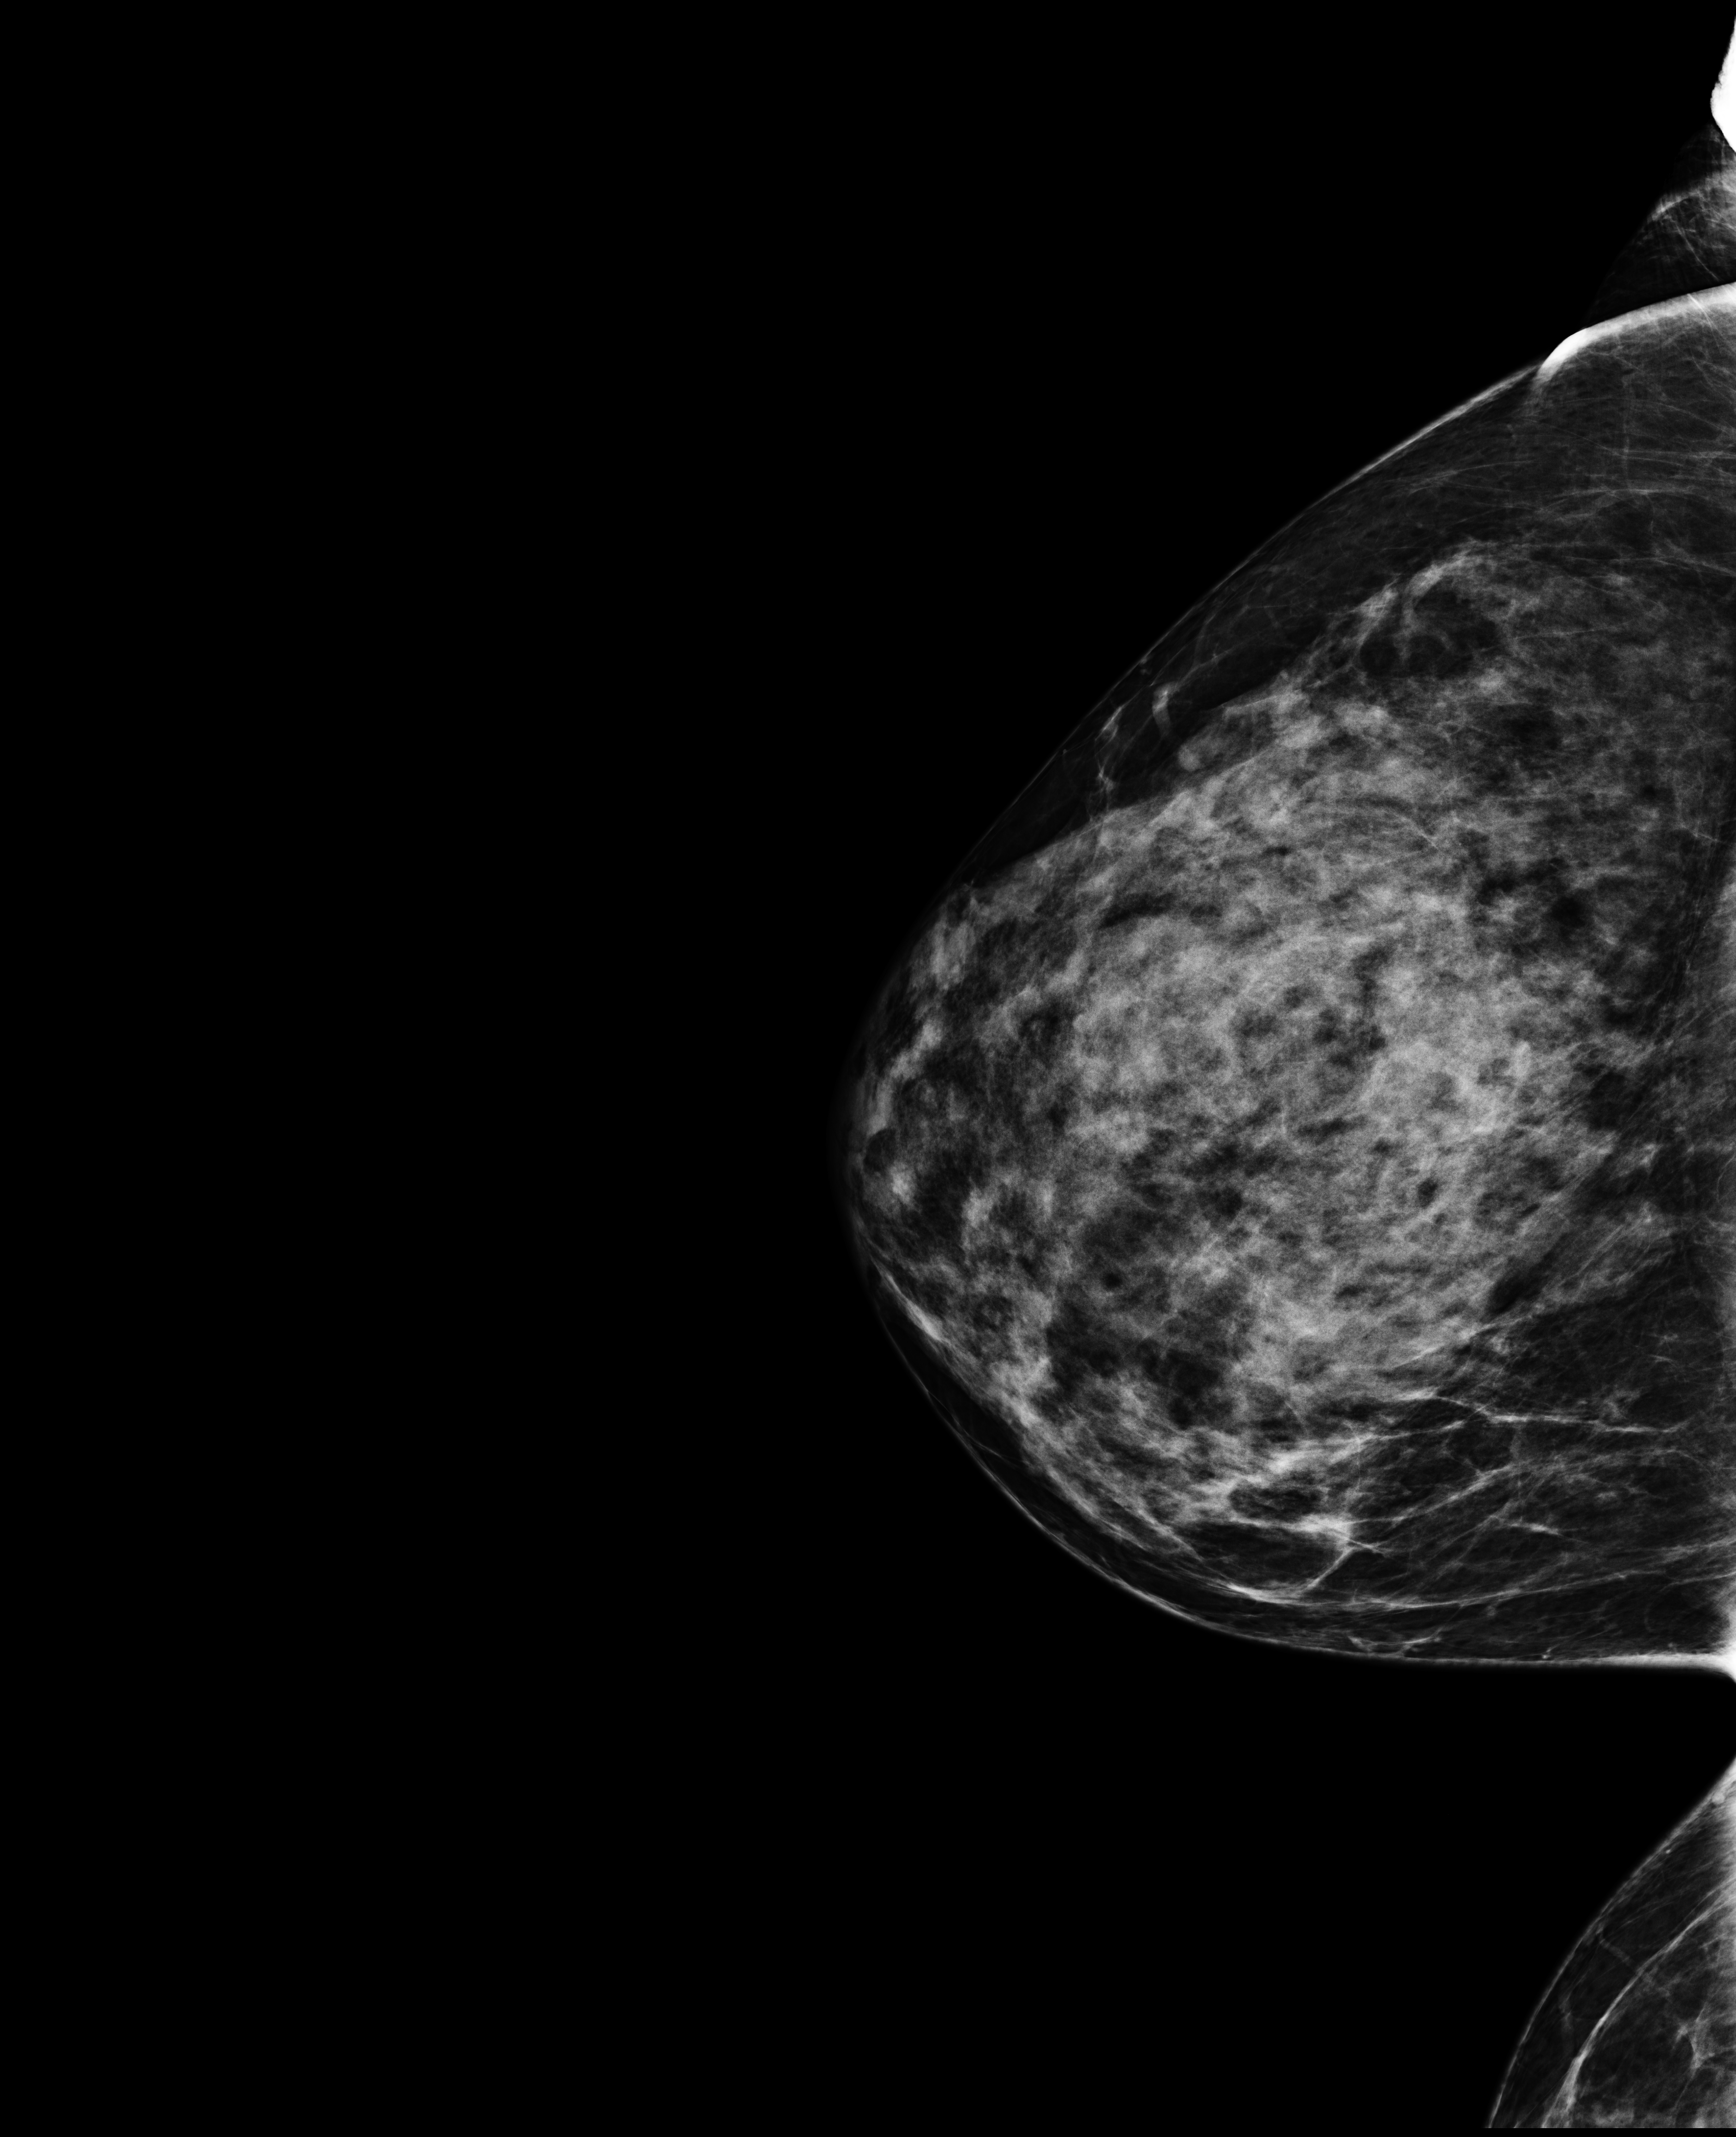
Screening examination; compressed breast thickness 80 mm. Patient aged 43 years (female).
Image type: full-field digital mammogram. Breast: right. Projection: CC view.